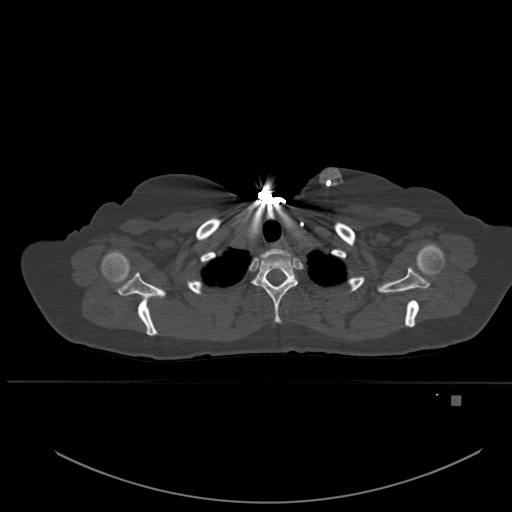
CT including the spine, one axial slice. Slice 418 of 651 in the series (ordered by position). Bone window (W 1800 / L 400 HU). 1.5 mm slice thickness. 512 × 512 image matrix, field of view 443 × 443 mm. Female patient, age 49 years. Case-level facts recorded for this patient, not image findings: primary cancer: breast.
Structures marked on this image (semi-automatically segmented with operator editing):
- T1 vertebra: bounding box (x1, y1, x2, y2) in pixels: (252, 251, 298, 324)